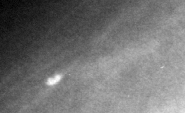
Region of interest cut from a scanned film mammogram (one marked finding); right breast; CC view; BI-RADS breast density category 1 (scale 1–4).
Finding: calcifications, morphology lucent center; BI-RADS assessment category 2; subtlety rating 3 on a 1 (subtle) to 5 (obvious) scale; benign without callback (not worked up further).